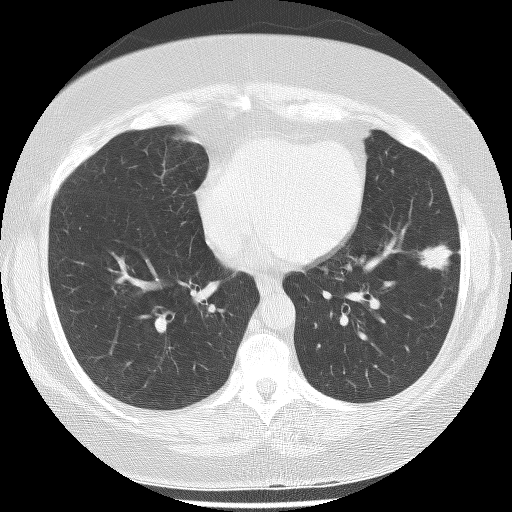
Axial slice from a low-dose chest CT screening exam, baseline annual screen, lung window (W 1500 / L -600 HU), lung (sharp) reconstruction kernel (BONE), 120 kVp. Female, age 56 years at enrolment.
• Lesion marked by an expert reader, bounding box <396,228,464,283> (left, top, right, bottom; pixels).
• The exam's reader record, not a measurement of the box and not confirmed to be the same lesion: non-calcified nodule or mass ≥4 mm, left lower lobe, 22 × 17 mm, spiculated (stellate) margins, soft tissue attenuation.